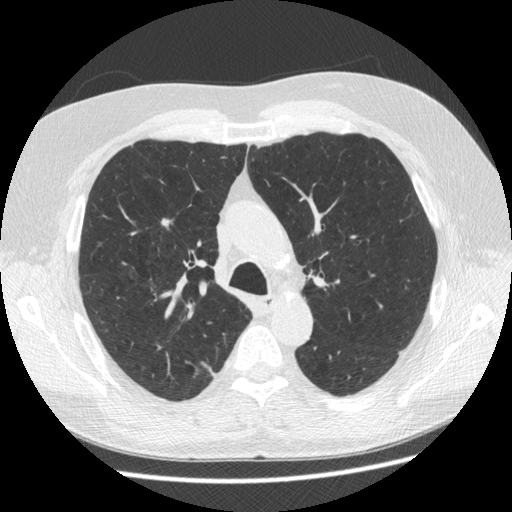
Low-dose screening chest CT, axial slice. Third screening round (two years after baseline). Lung window (W 1500 / L -600 HU). Slice 161 of 545 in the series. 512 × 512 image matrix, field of view 360 × 360 mm. Male participant, aged 63 years at enrolment. Former smoker at enrolment.
Lesion marked by an expert reader, bounding box <150,208,183,237> (left, top, right, bottom; pixels). The screening reader recorded 2 non-calcified nodules or masses ≥4 mm on this exam (right upper lobe, left upper lobe); which of them this box marks is not recorded. Later outcome: lung cancer diagnosed 342 days after this screen — adenocarcinoma, NOS, right upper lobe, stage IIA (AJCC 6th edition), 8 mm at pathology.